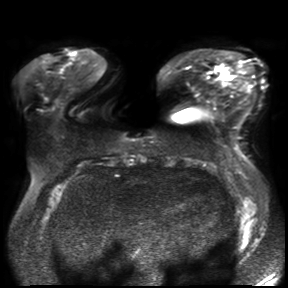
Breast MRI, one axial slice. Position 7 of 30 along the scan axis. Diffusion-weighted series; image 2 of 4 stored at this slice position (different b-values; order by instance number). 3 T. 288 × 288 image matrix, field of view 360 × 360 mm. Female patient.
Annotated regions visible in this slice (manually delineated by an expert):
- tumour on diffusion-weighted imaging: box from (x=219, y=64) to (x=228, y=72) px